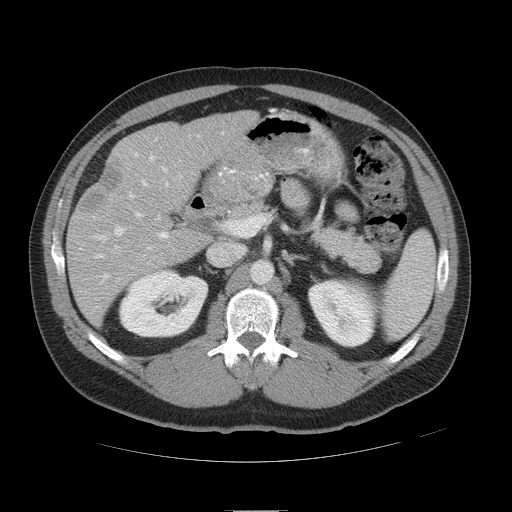
Contrast-enhanced abdominal CT, one axial slice. Slice 26 of 49 in the series (ordered by position). Soft-tissue window (W 400 / L 40 HU). 5 mm slice thickness. 512 × 512 image matrix, field of view 425 × 425 mm. Male patient, age 52 years. Case-level facts recorded for this patient, not image findings: diagnosis: colorectal cancer liver metastases, imaged before liver resection; multiple liver metastases: yes; largest metastasis: 5.1 cm; disease in both lobes: yes.
Annotated regions visible in this slice (manually delineated by an expert):
- hepatic veins: bounding box (x1, y1, x2, y2) in pixels: (114, 156, 168, 250)
- liver: (69, 112, 252, 321)
- planned liver remnant (the part of the liver to remain after resection): (132, 112, 252, 191)
- portal vein (with intrahepatic branches): (94, 192, 169, 259)
- liver metastasis: (84, 168, 121, 212)